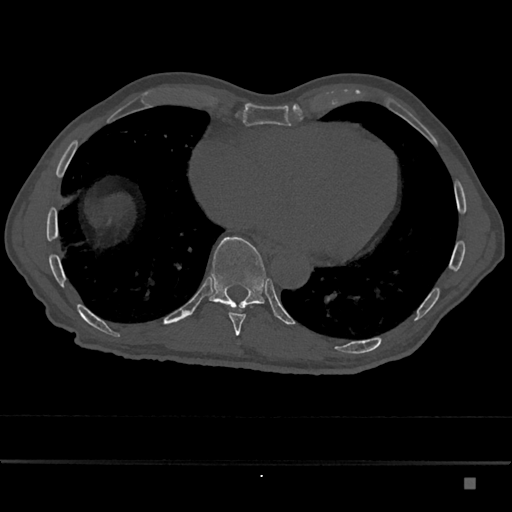
CT including the spine, one axial slice; position 771 of 797 along the scan axis; reconstruction kernel Br40s/3; bone window (W 1800 / L 400 HU); 0.5 mm slice thickness; 512 × 512 image matrix, field of view 390 × 390 mm. Male patient, age 72 years. From the clinical record (not read from this slice): primary cancer: prostate.
Outlined on this slice (semi-automatically segmented with operator editing):
- T10 vertebra: bounding box <209,237,266,310> (left, top, right, bottom; pixels)
- T9 vertebra: <229,305,248,336>